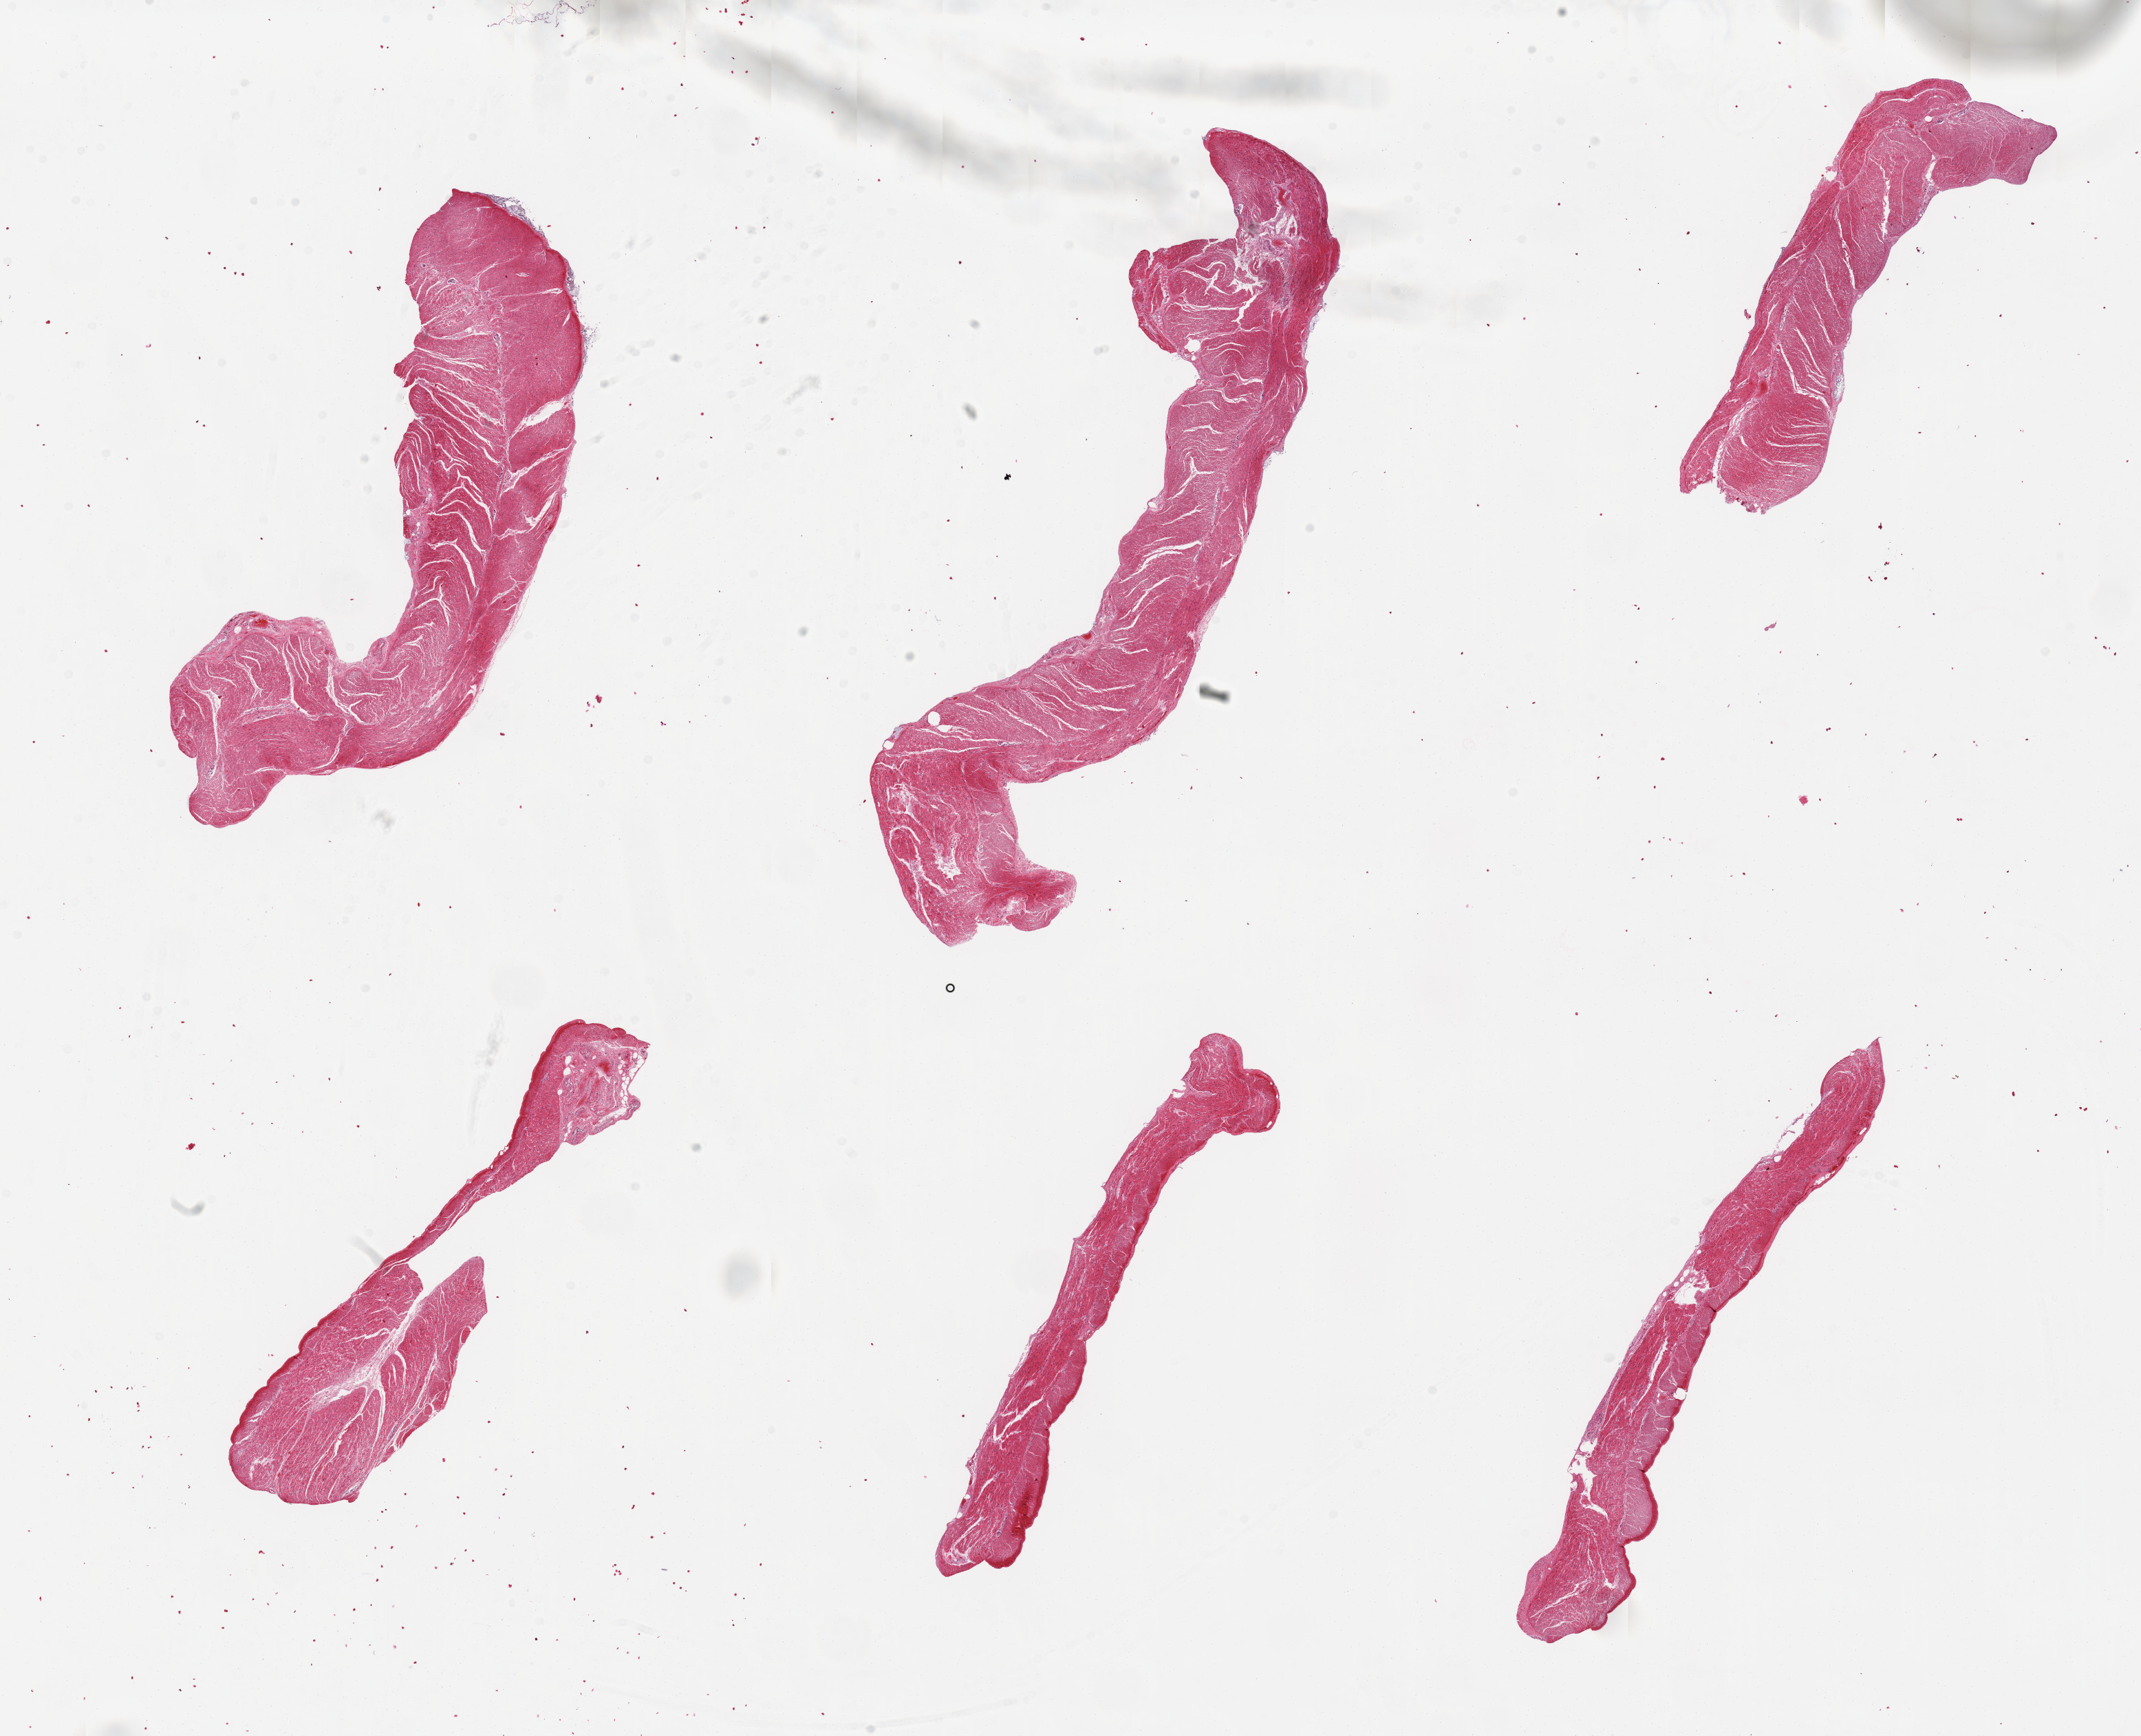
H&E whole-slide image, shown as a low-resolution overview of the whole scanned area (about 24.6 x 20.0 mm, acquisition: 20x scan), PAXgene-fixed paraffin-embedded (PFPE) section, target tissue: sigmoid colon, tissue donor sample. Male donor.
Pathologist's review note for this sample: 6 pieces; muscularis.